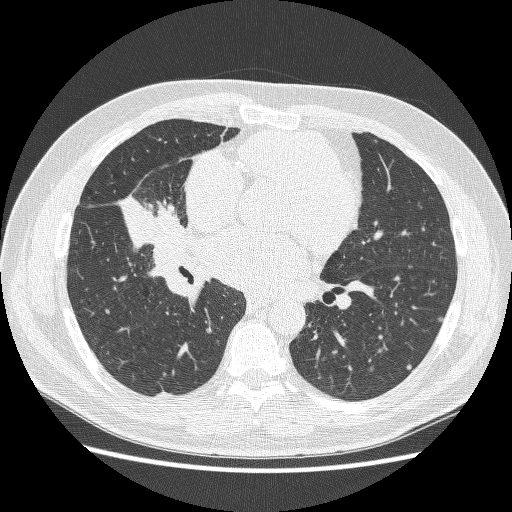
Axial slice from a low-dose chest CT screening exam. Baseline annual screen. Lung window (W 1500 / L -600 HU). Lung (sharp) reconstruction kernel (BONE). Male, age 59 years at enrolment. Former smoker at enrolment.
• Lesion marked by an expert reader, bounding box [x1, y1, x2, y2] px = [117, 176, 197, 255].
• No non-calcified nodule or mass ≥4 mm was recorded by the screening reader at this exam.
• Participant outcome: lung cancer diagnosed 24 days after this screen — adenocarcinoma, NOS, right middle lobe, poorly differentiated (G3), stage IV (AJCC 6th edition), 54 mm at pathology.